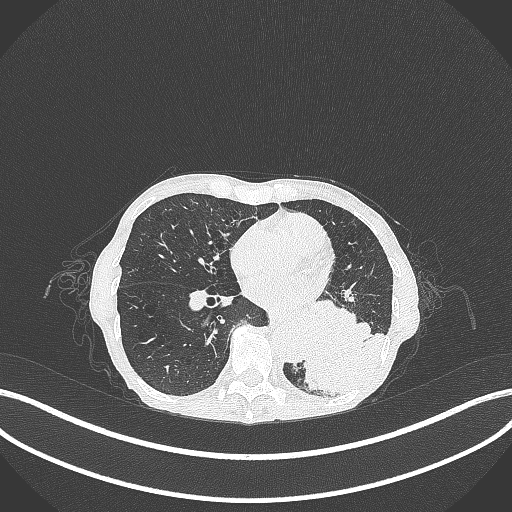
Chest CT, one axial slice; position 113 of 347 along the scan axis; lung window (W 1500 / L -600 HU); 1 mm slice thickness; 512 × 512 image matrix, field of view 400 × 400 mm. Patient: female, 70 years. From the clinical record (not read from this slice): clinical TNM (as recorded): T3 N0 M0; histopathological grade: G3.
Structures marked on this image (rectangle marked by the reading radiologist):
- lung tumour (recorded histology: small cell carcinoma): bounding box <292,307,392,399> (left, top, right, bottom; pixels)